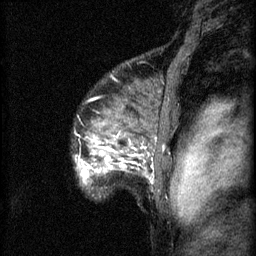
Breast MRI (dynamic contrast-enhanced), one sagittal slice; position 52 of 60 along the scan axis; 3 images stored at this slice position (order not interpretable as contrast timing); 1.5 T; TE 4.2 ms, TR 8.2 ms; 256 × 256 image matrix, field of view 180 × 180 mm. Patient: female, 48 years.
Annotated regions visible in this slice (semi-automatic segmentation, software-assisted and operator-edited):
- analysis volume of interest (the breast-tissue region the enhancement analysis was run in; not a lesion): bounding box (x1, y1, x2, y2) in pixels: (78, 138, 153, 189)
- tumour enhancement mask (voxels above the 70 % enhancement threshold inside the analysis volume of interest): (81, 156, 126, 181)